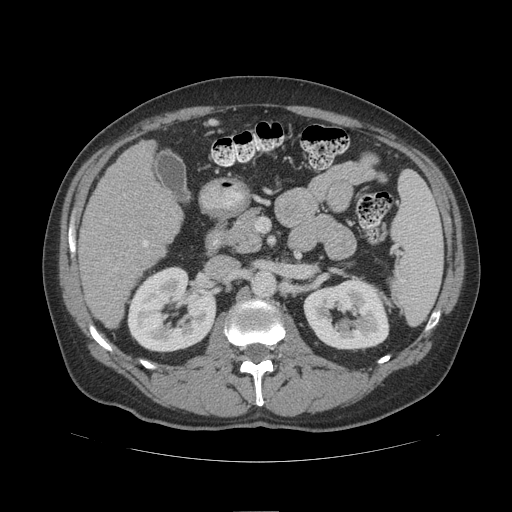
Contrast-enhanced abdominal CT (liver protocol), one axial slice; slice 50 of 109 in the series (ordered by position); soft-tissue window (W 400 / L 40 HU); 2.5 mm slice thickness; 512 × 512 image matrix, field of view 420 × 420 mm. Case-level facts recorded for this patient, not image findings: diagnosis: hepatocellular carcinoma (patient treated with transarterial chemoembolisation; whether this scan precedes or follows treatment is not stated here); TNM stage (as recorded): Stage-IIIB; Child-Pugh class: A; tumour differentiation: poorly differentiated.
Outlined on this slice (semi-automatically segmented with operator editing):
- liver parenchyma outside the tumour (the mass and vessels are separate outlines, so this box may not span the whole liver): bounding box (x1, y1, x2, y2) in pixels: (80, 140, 182, 328)
- liver vessels: (143, 240, 148, 247)